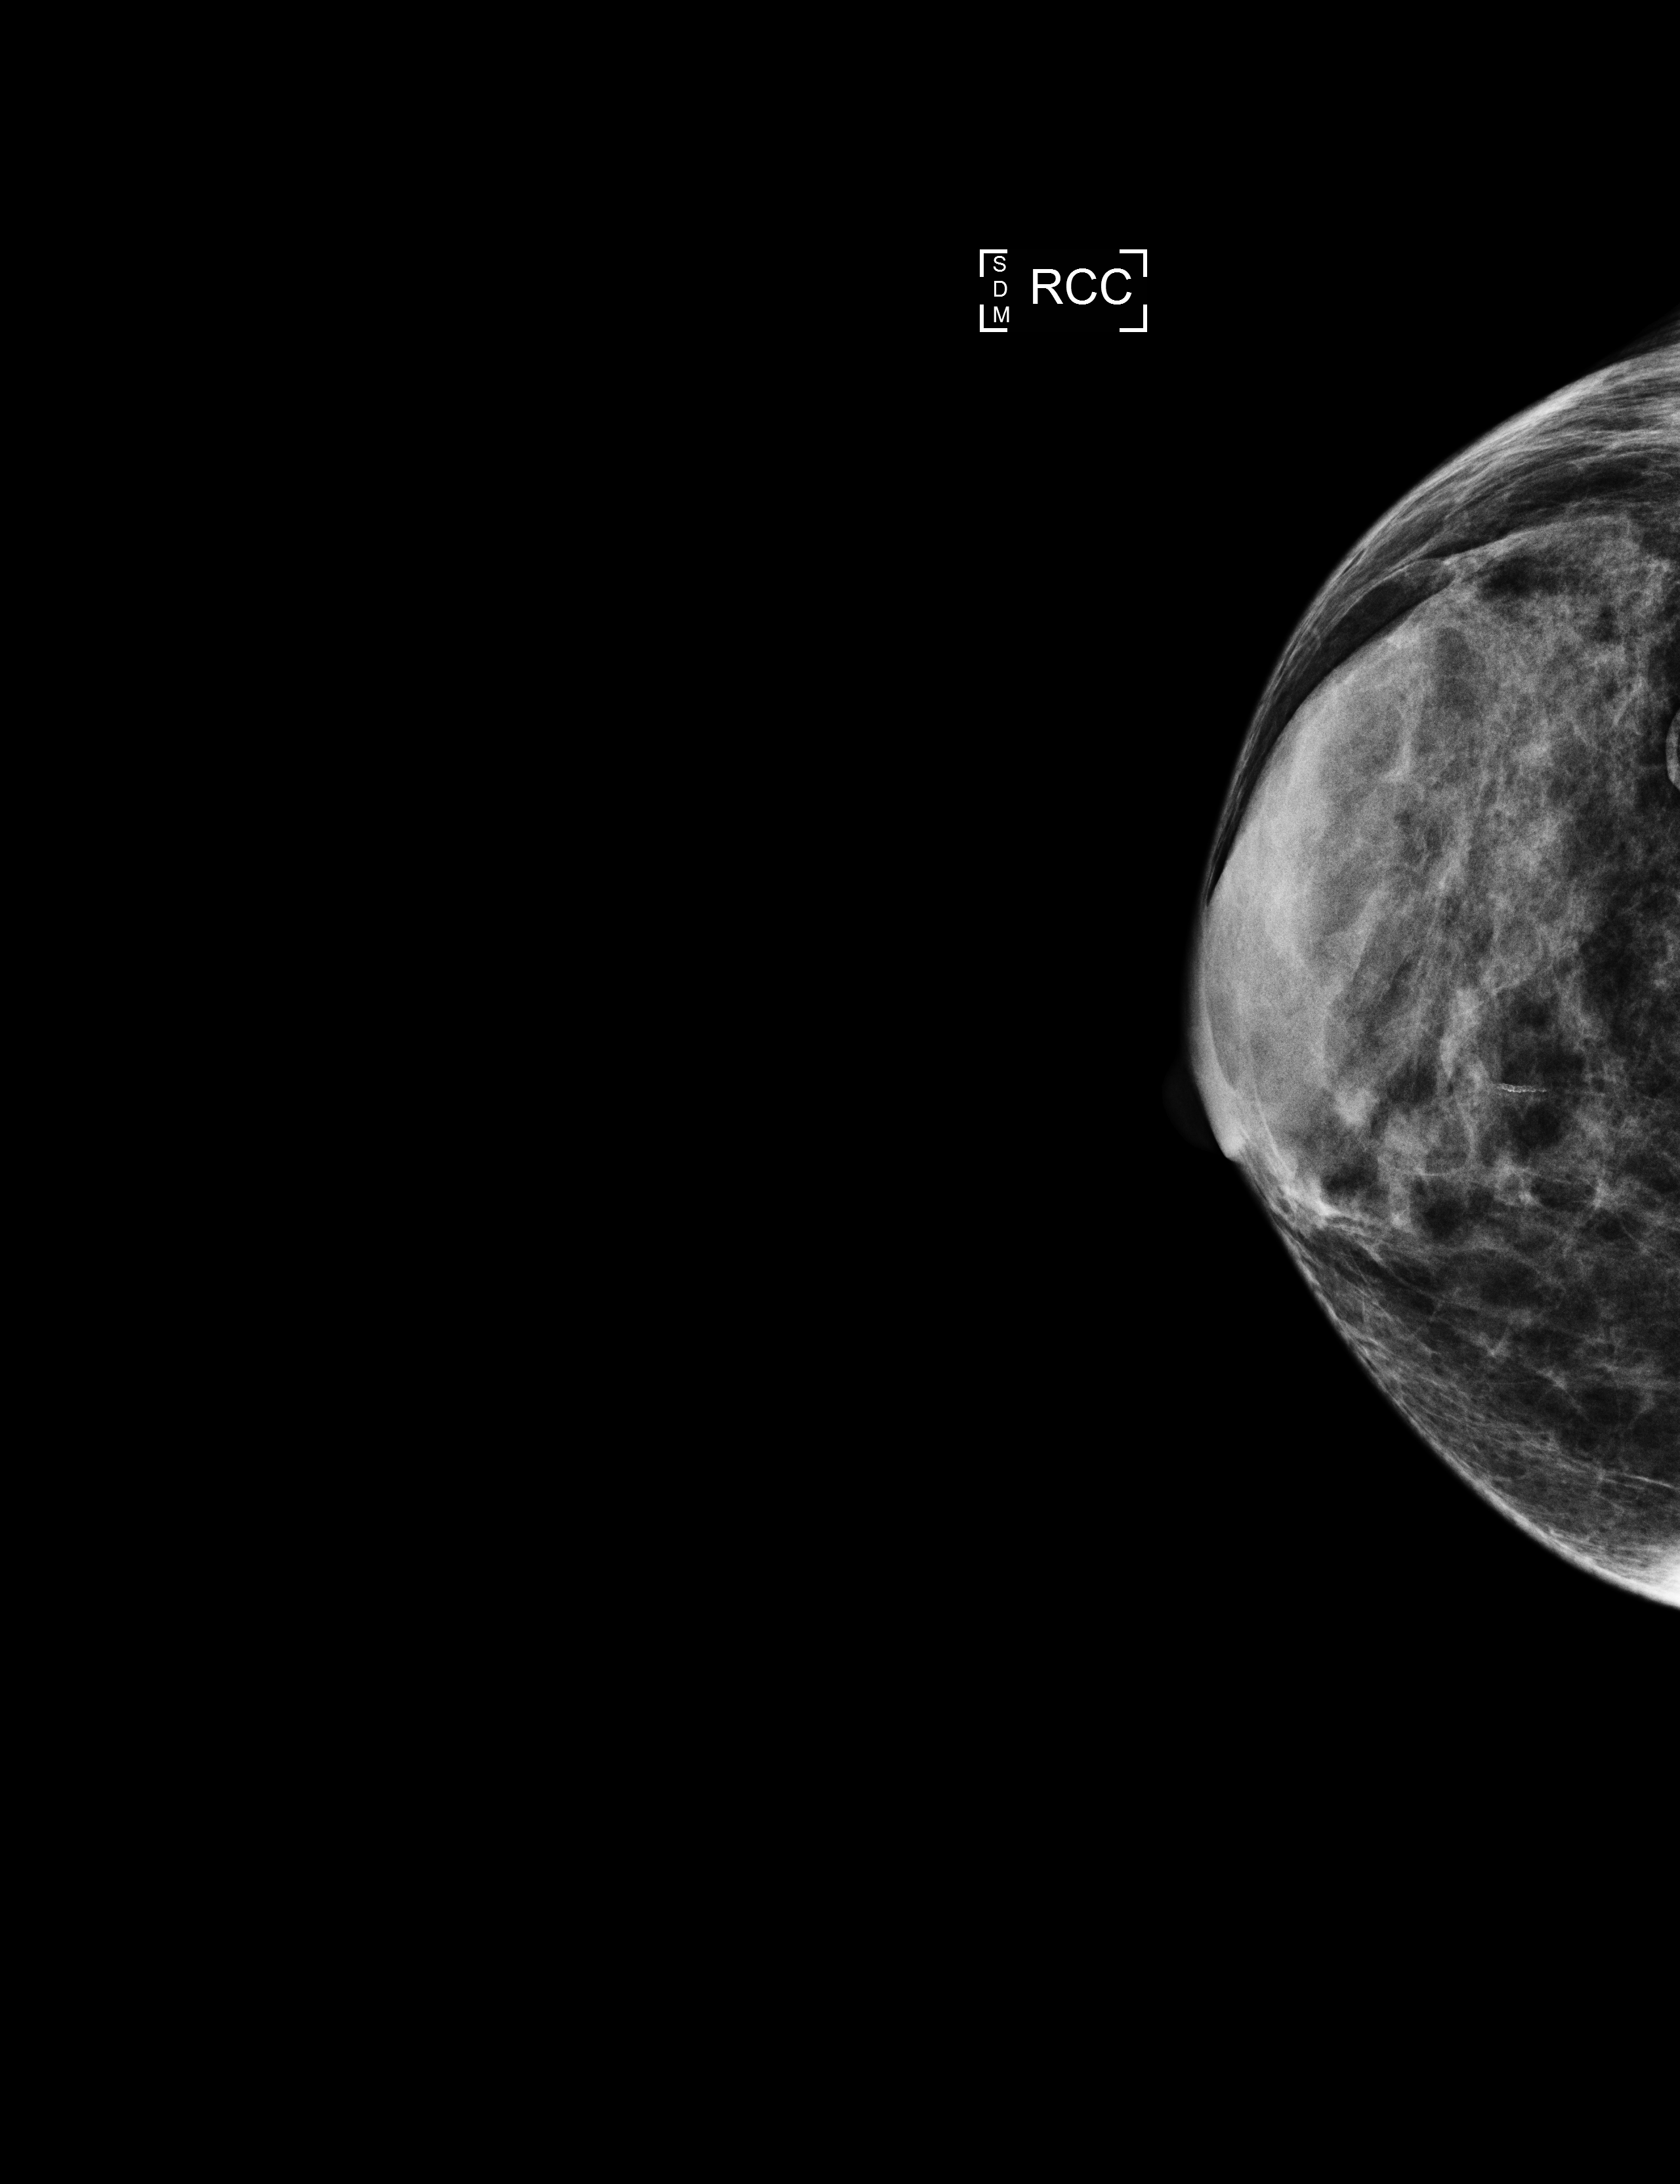
Full-field digital mammogram (FFDM), right breast, cranio-caudal projection, annual screening mammography examination, compressed breast thickness 37 mm. Patient: female, 66 years.
- breast density at the screening exam (both breasts): heterogeneously dense (BI-RADS density category c)
- final BI-RADS assessment for this screening round (tomosynthesis exam, both breasts): category 1
- recall: no recall after this screen